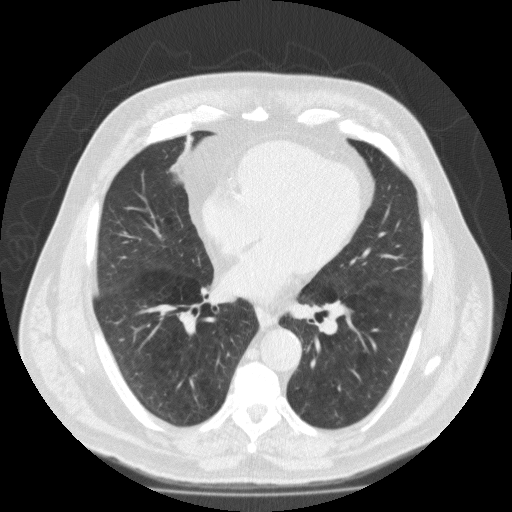
Low-dose screening chest CT, one axial slice; position 90 of 188 along the scan axis; reconstruction kernel FC10; 120 kVp; lung window (W 1500 / L -600 HU); 2 mm slice thickness; 512 × 512 image matrix.
Outlined on this slice (manually delineated by an expert):
- lesion 1 (tumor, lower lobe of right lung): bounding box [x1, y1, x2, y2] px = [171, 135, 195, 184]